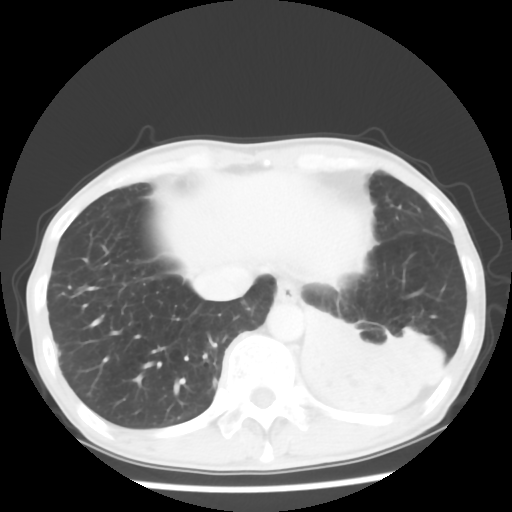
Chest CT, one axial slice. Slice 12 of 64 in the series (ordered by position). Lung window (W 1500 / L -600 HU). 5 mm slice thickness. 512 × 512 image matrix. Male patient, age 68 years. From the clinical record (not read from this slice): clinical TNM (as recorded): T4 N0 M0.
Outlined on this slice (bounding box drawn by a radiologist):
- lung tumour (recorded histology: squamous cell carcinoma): box from (x=289, y=303) to (x=456, y=423) px